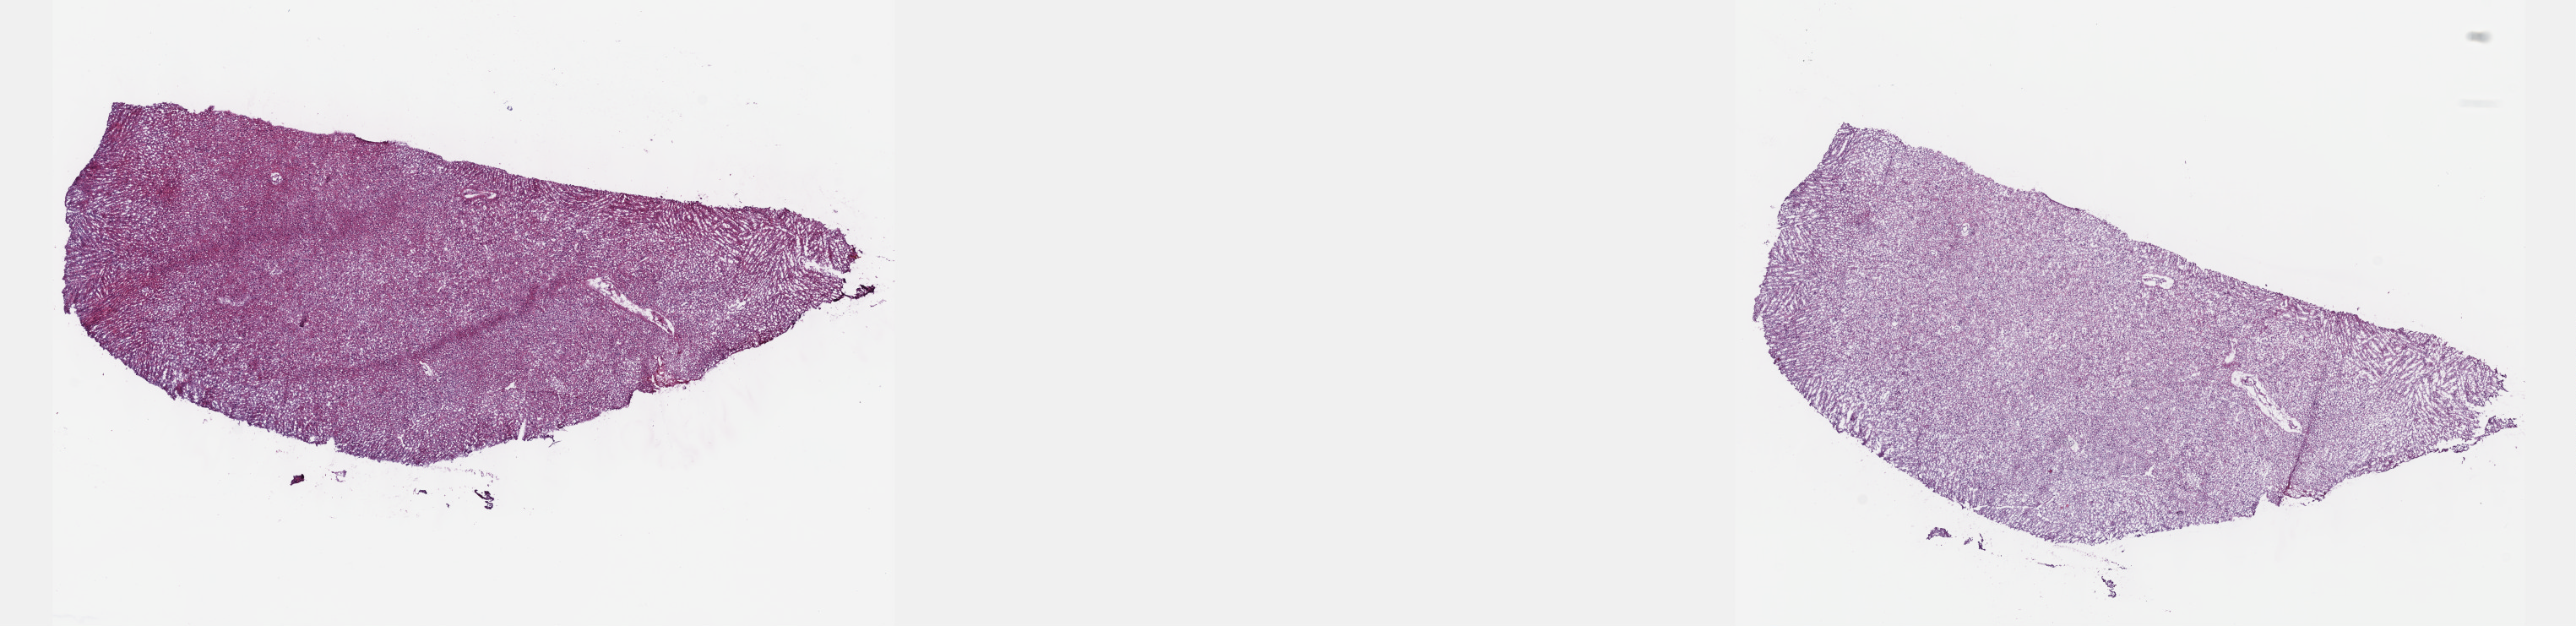
Digitized Hematoxylin and eosin (H&E) stained tissue section (whole slide) — a low-resolution overview of the entire scanned area, about 24.6 x 6.0 mm. Frozen section from the top of the tissue portion. Brain, primary tumour sample. Male patient; age at initial diagnosis 50 years. Histologic grade: G2 (moderately differentiated). Pathologist review of this section (percent, as recorded): tumour cells 50%, tumour nuclei 90%, normal cells 10%, stromal cells 40%, necrosis 0%. Inflammatory infiltration, as recorded: lymphocyte infiltration 0%, monocyte infiltration 0%, neutrophil infiltration 0%.
• pathologic diagnosis: Oligodendroglioma, NOS (cerebrum)